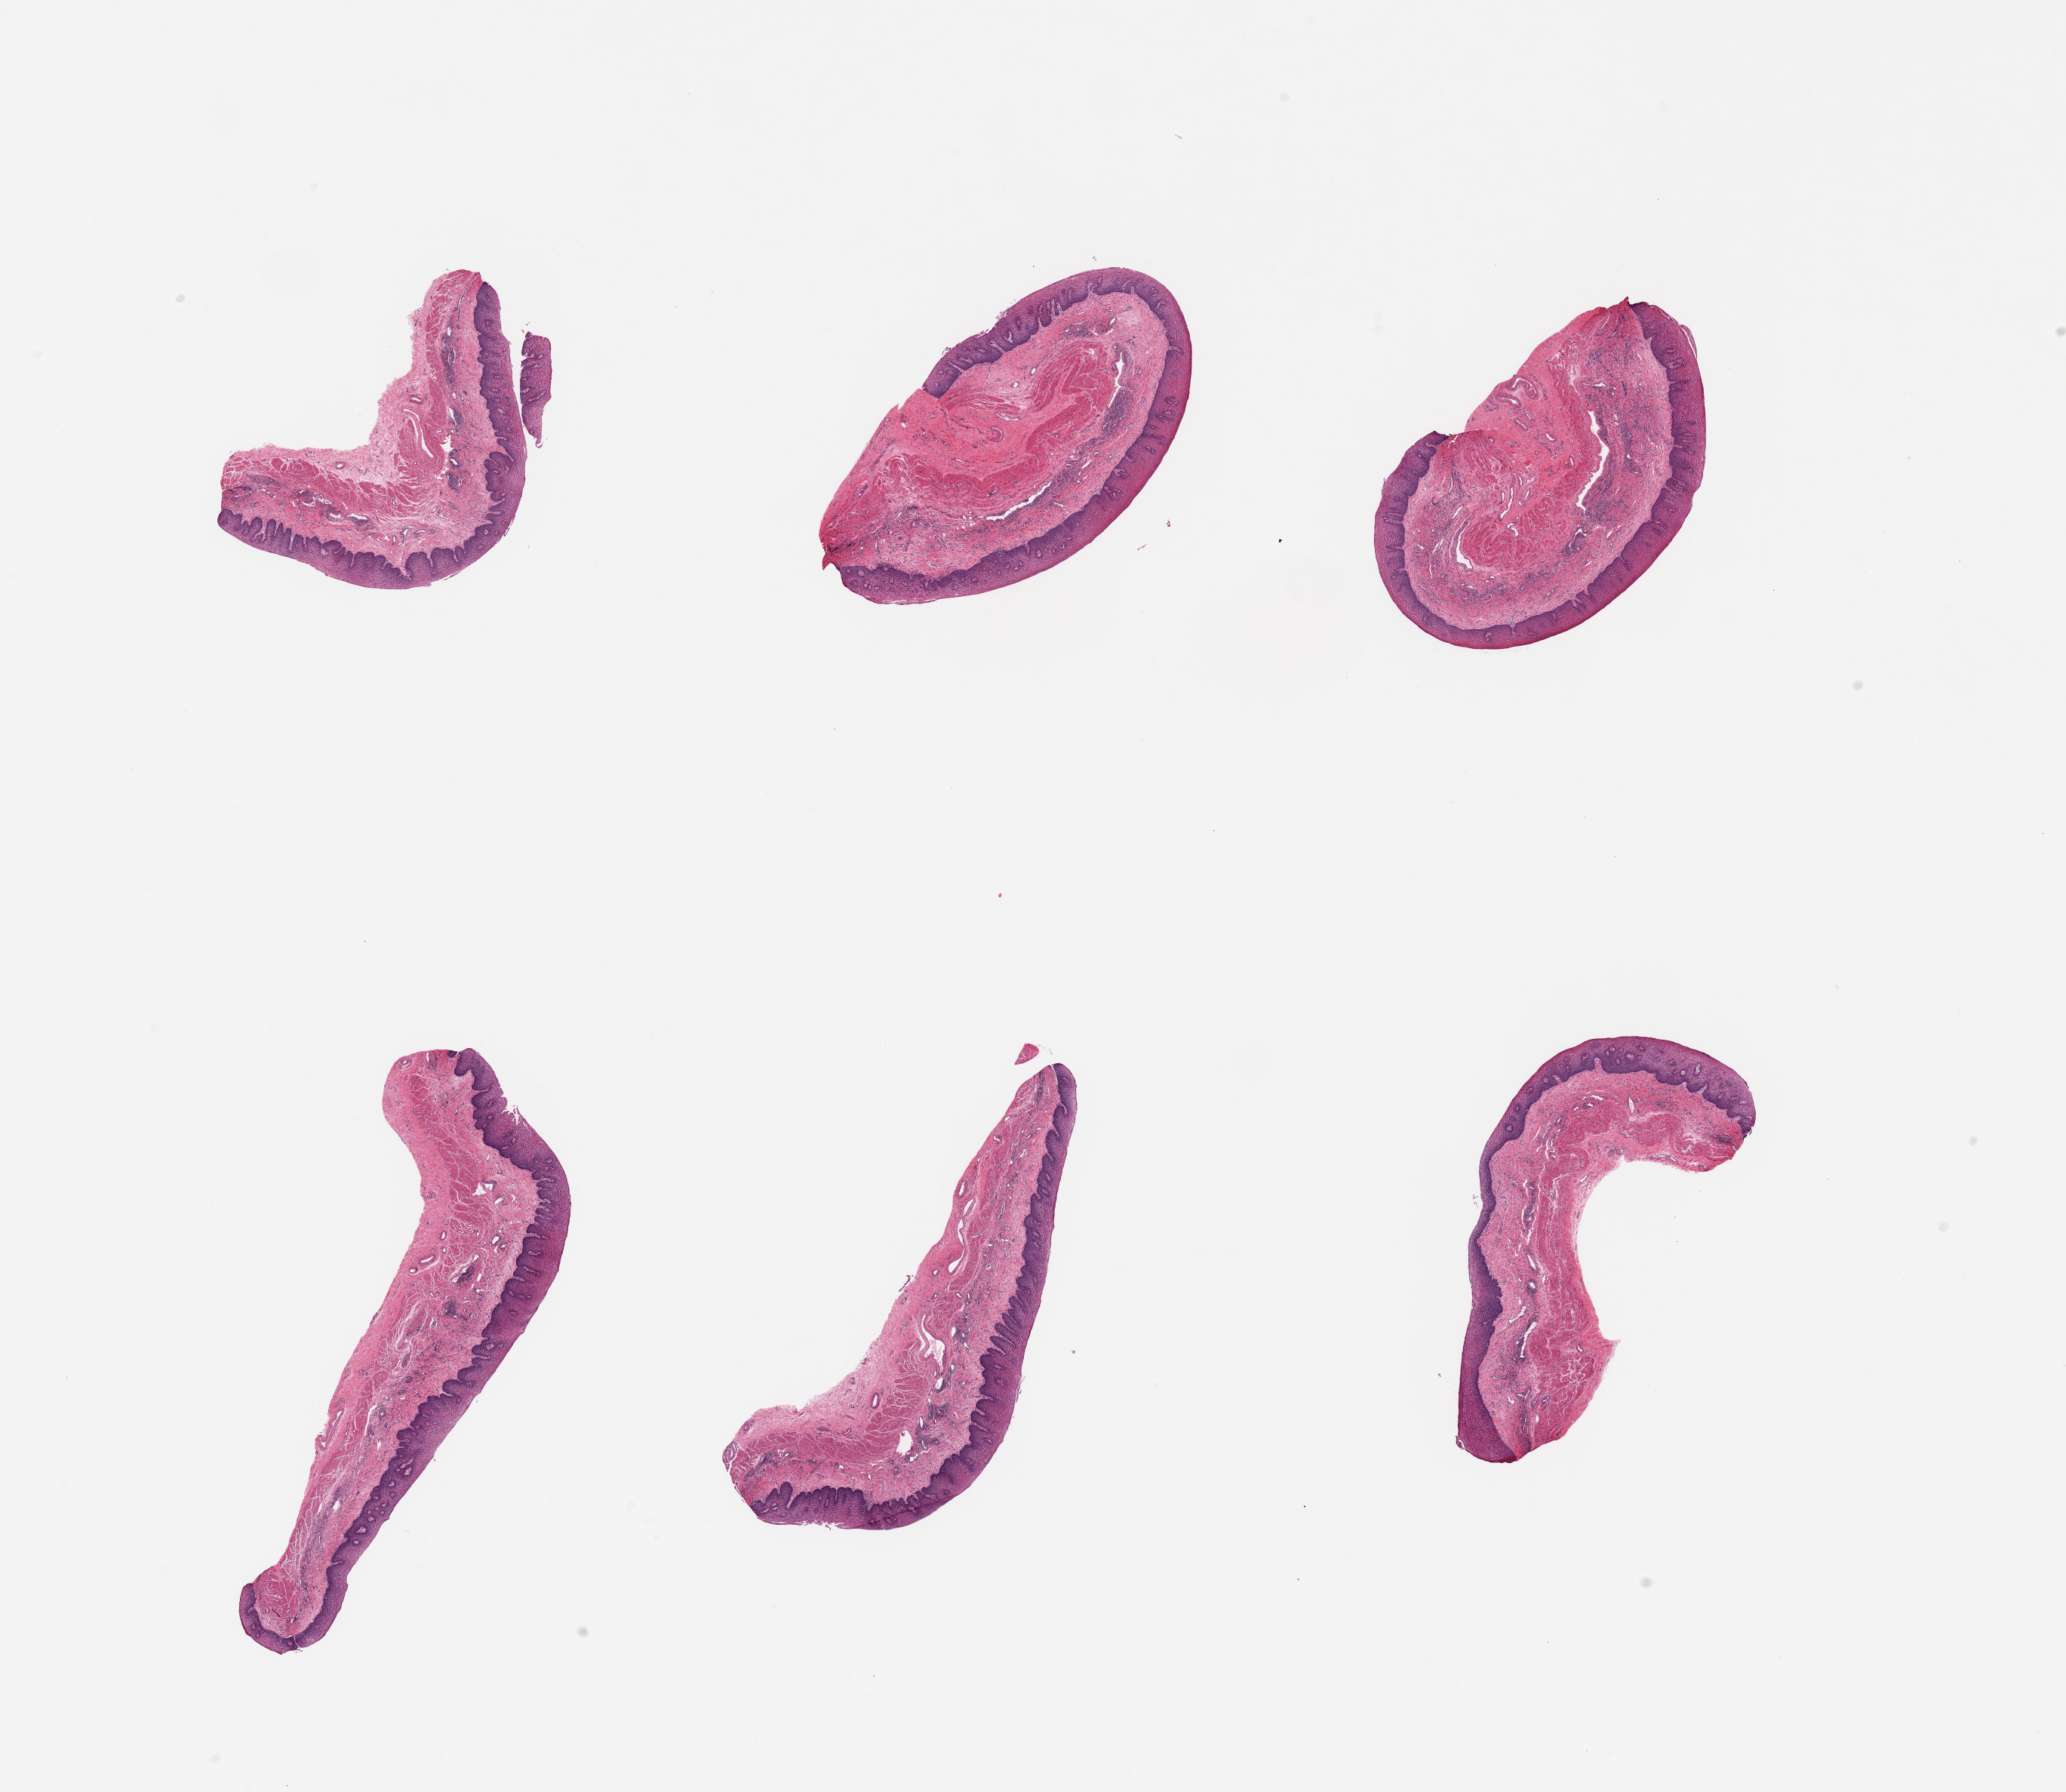
Hematoxylin and eosin (H&E) whole-slide image — a low-resolution overview of the entire scanned area, about 21.7 x 18.8 mm. PAXgene-fixed paraffin-embedded (PFPE) section. Section of esophageal mucous membrane (target tissue). Tissue donor sample. Donor: male.
Pathologist's review note for this sample: 6 pieces, squamous mucosa up to ~0.35mm, 10-20% of thickness.